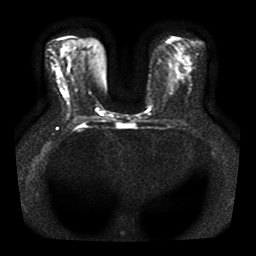
Breast MRI, one axial slice. Position 22 of 41 along the scan axis. Diffusion-weighted series; image 2 of 4 stored at this slice position (different b-values; order by instance number). 1.5 T. 5 mm slice thickness. 256 × 256 image matrix, field of view 330 × 330 mm. Female patient.
Outlined on this slice (manually delineated by an expert):
- tumour on diffusion-weighted imaging: bounding box (x1, y1, x2, y2) in pixels: (61, 89, 64, 95)